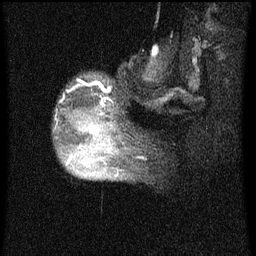
Breast MRI (dynamic contrast-enhanced), one sagittal slice. Position 16 of 60 along the scan axis. Dynamic contrast-enhanced series, image 2 of 4 at this slice position (ordered by acquisition). 1.5 T. TE 4.2 ms, TR 8 ms. 2 mm slice thickness. 256 × 256 image matrix. Patient: female, 50 years.
Annotated regions visible in this slice (semi-automatic segmentation, software-assisted and operator-edited):
- analysis volume of interest (the breast-tissue region the enhancement analysis was run in; not a lesion): bounding box [x1, y1, x2, y2] px = [57, 78, 124, 177]
- tumour enhancement mask (voxels above the 70 % enhancement threshold inside the analysis volume of interest): [70, 126, 100, 161]